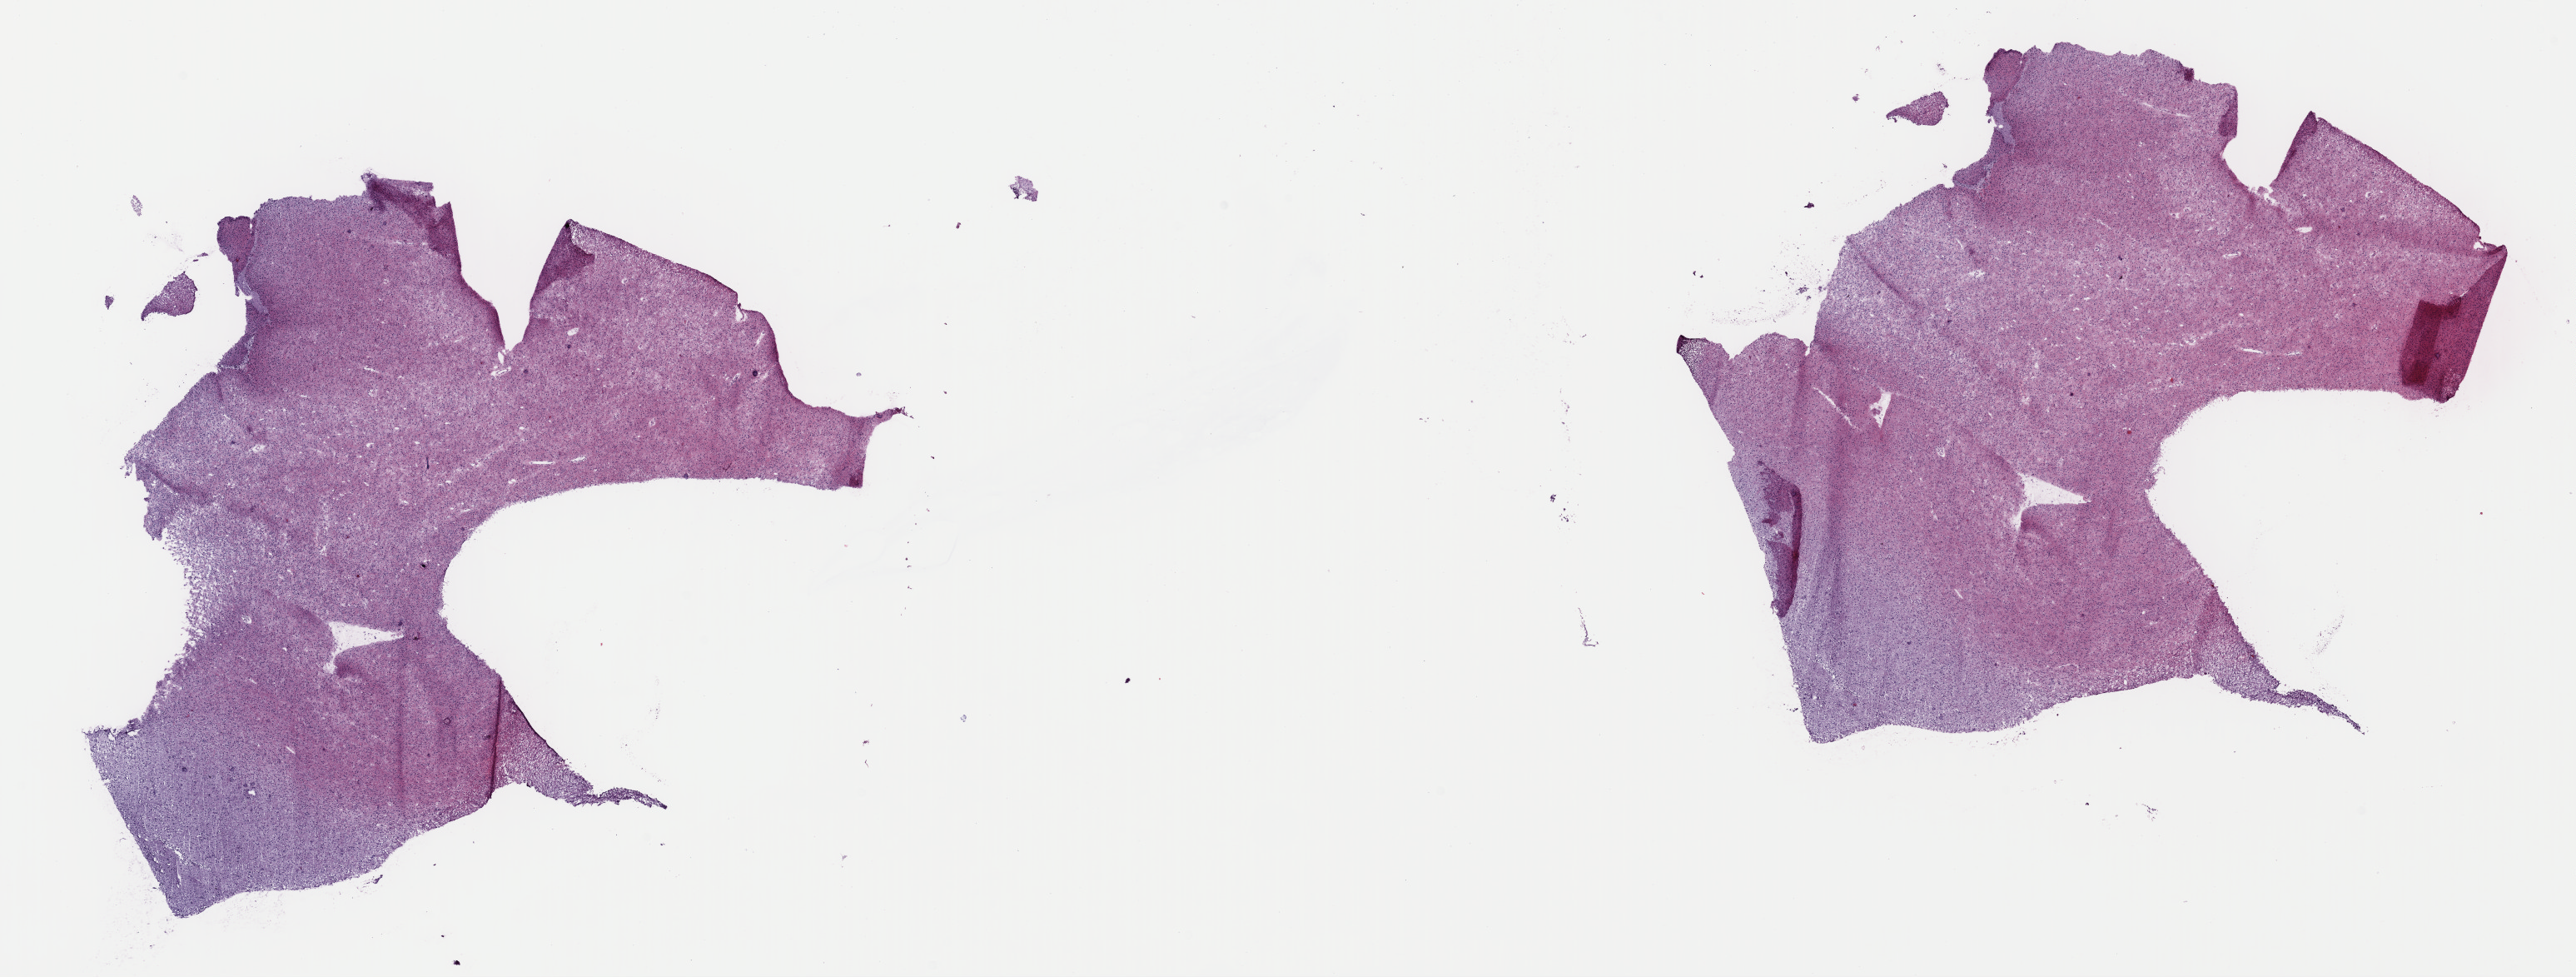
H&E-stained whole-slide image, low-resolution overview of the scanned area, about 24.4 x 9.3 mm (slide scanned at 40x), frozen section from the top of the tissue portion, primary tumour sample from the brain. Male patient; age at initial diagnosis 58 years. Composition of this section per pathologist review: tumour cells 60%, tumour nuclei 90%.
Histologic diagnosis: Oligodendroglioma, anaplastic (cerebrum).